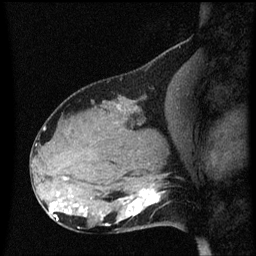
Breast MRI (dynamic contrast-enhanced), one sagittal slice. Position 26 of 60 along the scan axis. Dynamic contrast-enhanced series, image 2 of 3 at this slice position (ordered by acquisition). 1.5 T. TE 4.2 ms, TR 8.4 ms. 2 mm slice thickness. 256 × 256 image matrix, field of view 200 × 200 mm. Female patient, age 31 years. Case-level facts recorded for this patient, not image findings: setting: breast cancer imaged before/during neoadjuvant chemotherapy; receptor status: HR-positive, HER2-negative.
Outlined on this slice (semi-automatic segmentation, software-assisted and operator-edited):
- analysis volume of interest (the breast-tissue region the enhancement analysis was run in; not a lesion): bounding box (x1, y1, x2, y2) in pixels: (102, 166, 176, 229)
- tumour enhancement mask (voxels above the 70 % enhancement threshold inside the analysis volume of interest): (102, 190, 161, 225)